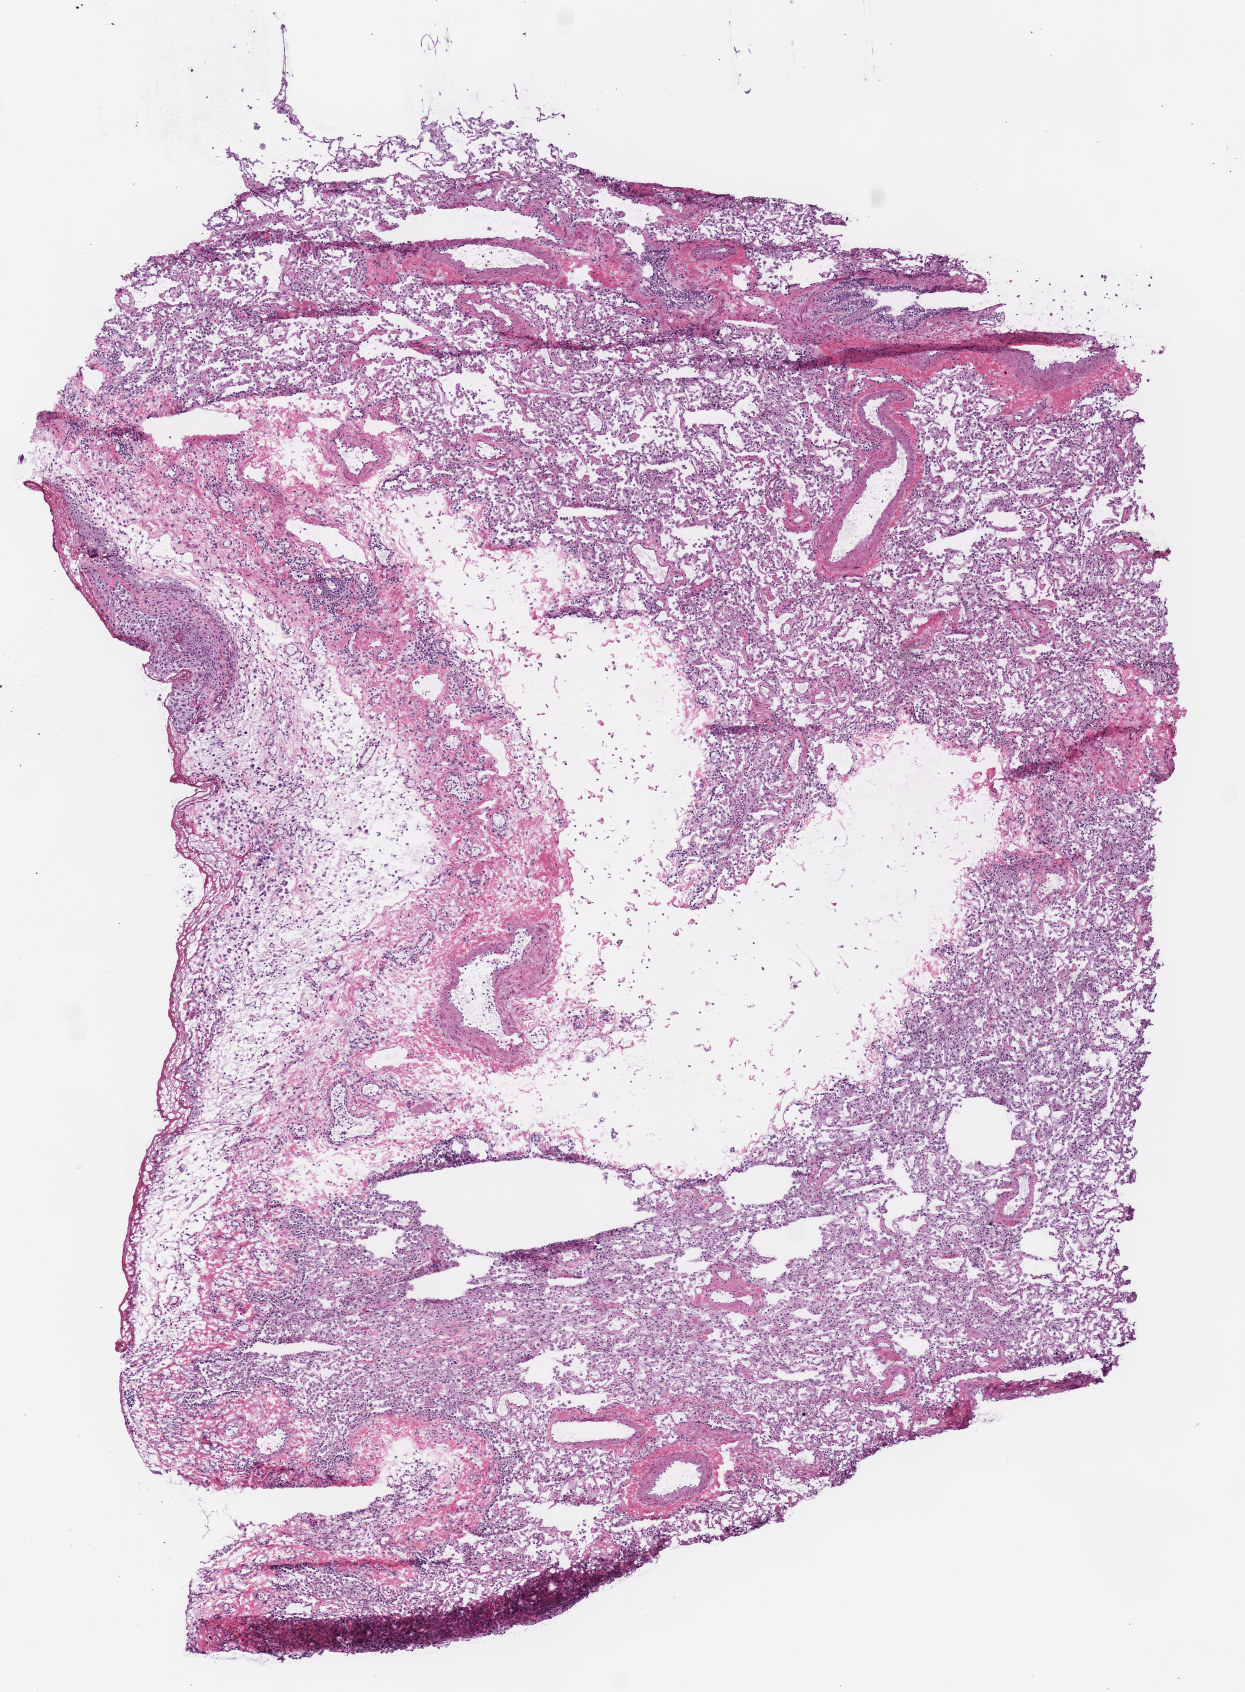
H&E whole-slide image, shown as a low-resolution overview of the whole scanned area (about 4.9 x 6.7 mm, acquisition: 40x scan). Frozen section. Lung, solid tissue normal (non-tumour tissue) sample. Male patient; age at initial diagnosis 60 years. Inflammatory infiltration, as recorded: lymphocyte infiltration 3%, monocyte infiltration 25%.
• this section: solid tissue normal sample (biorepository sample class)
• patient diagnosis: Squamous cell carcinoma, NOS (lower lobe, lung)